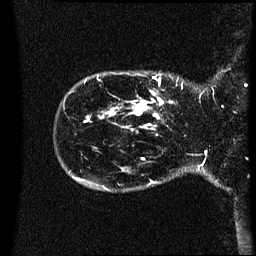
Breast MRI (dynamic contrast-enhanced), one sagittal slice. Position 6 of 60 along the scan axis. Dynamic contrast-enhanced series, image 2 of 3 at this slice position (ordered by acquisition). 1.5 T. TE 4.2 ms, TR 8.4 ms. 2.2 mm slice thickness. 256 × 256 image matrix, field of view 220 × 220 mm. Patient: female, 41 years. From the clinical record (not read from this slice): setting: breast cancer imaged before/during neoadjuvant chemotherapy; receptor status: HER2-positive.
Annotated regions visible in this slice (semi-automatically segmented with operator editing):
- analysis volume of interest (the breast-tissue region the enhancement analysis was run in; not a lesion): bounding box [x1, y1, x2, y2] px = [124, 80, 197, 119]
- tumour enhancement mask (voxels above the 70 % enhancement threshold inside the analysis volume of interest): [132, 90, 174, 119]